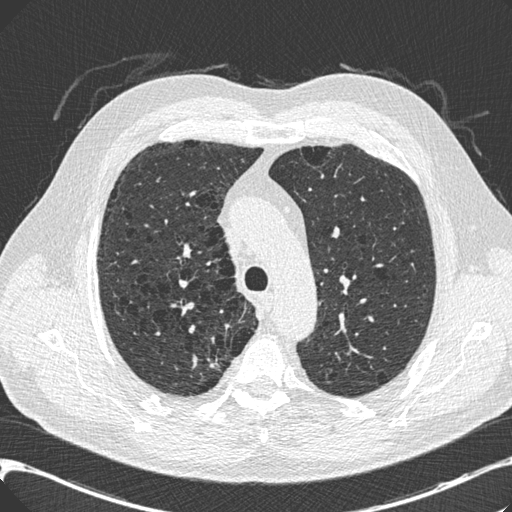
Low-dose screening chest CT, one axial slice. Position 145 of 197 along the scan axis. 120 kVp. Lung window (W 1500 / L -600 HU). 512 × 512 image matrix, field of view 367 × 367 mm.
Annotated regions visible in this slice (manually delineated by an expert):
- lesion 1 (tumor, upper lobe of right lung): box from (x=206, y=357) to (x=221, y=369) px